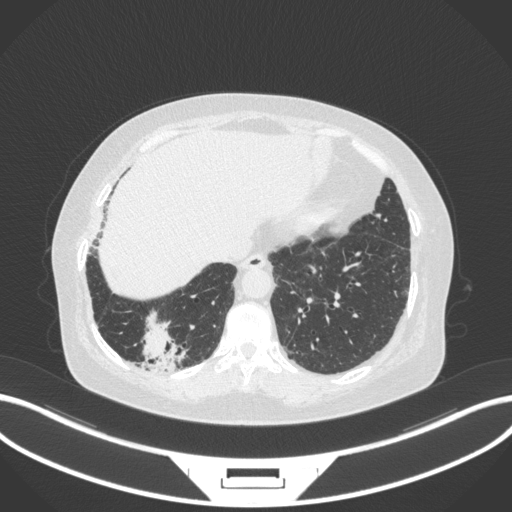
Chest CT, one axial slice. Slice 35 of 303 in the series (ordered by position). Reconstruction kernel B31f. Lung window (W 1500 / L -600 HU). 512 × 512 image matrix. Female patient, age 65 years. Case-level facts recorded for this patient, not image findings: clinical TNM (as recorded): T2b N1 M0; histopathological grade: G1.
Structures marked on this image (bounding box drawn by a radiologist):
- lung tumour (recorded histology: adenocarcinoma): bounding box <135,306,184,374> (left, top, right, bottom; pixels)